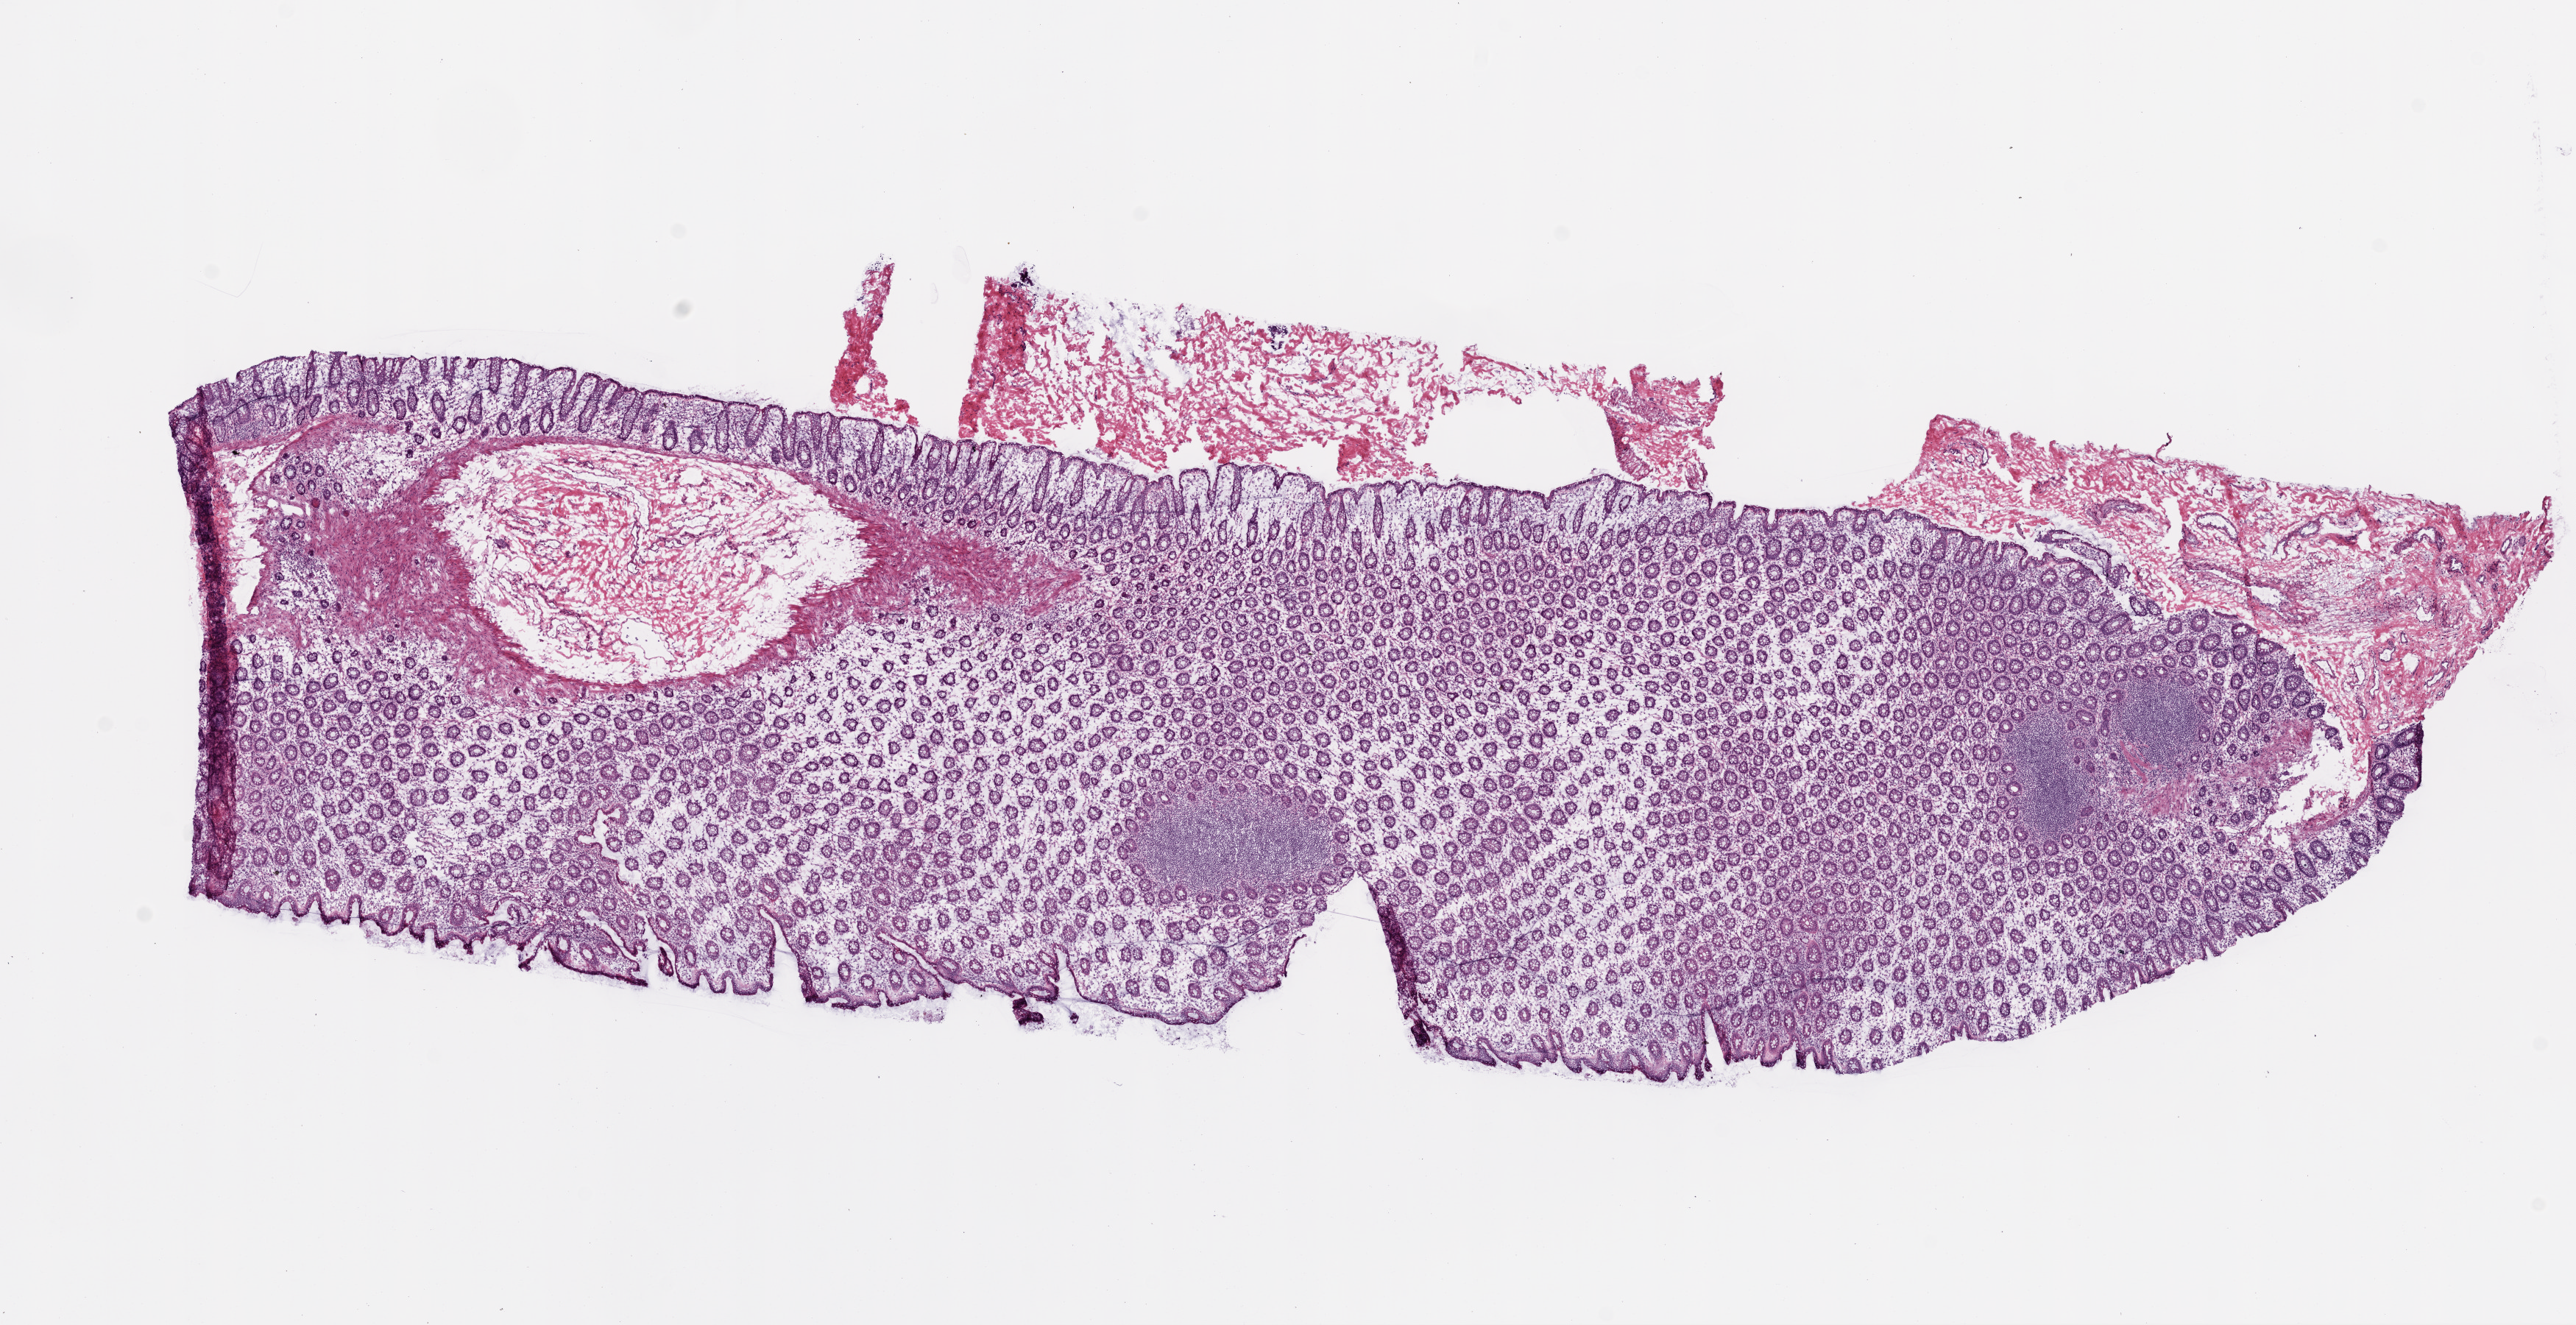
Digitized H&E tissue section (whole slide), a low-resolution overview of the entire scanned area, about 14.0 x 7.2 mm (from a 20x scan); frozen section from the top of the tissue portion; solid tissue normal (non-tumour tissue) sample from the colon. Patient: male, age at initial diagnosis 60 years.
This section: solid tissue normal (non-tumour) sample from the same patient. Patient diagnosis: Adenocarcinoma, NOS.